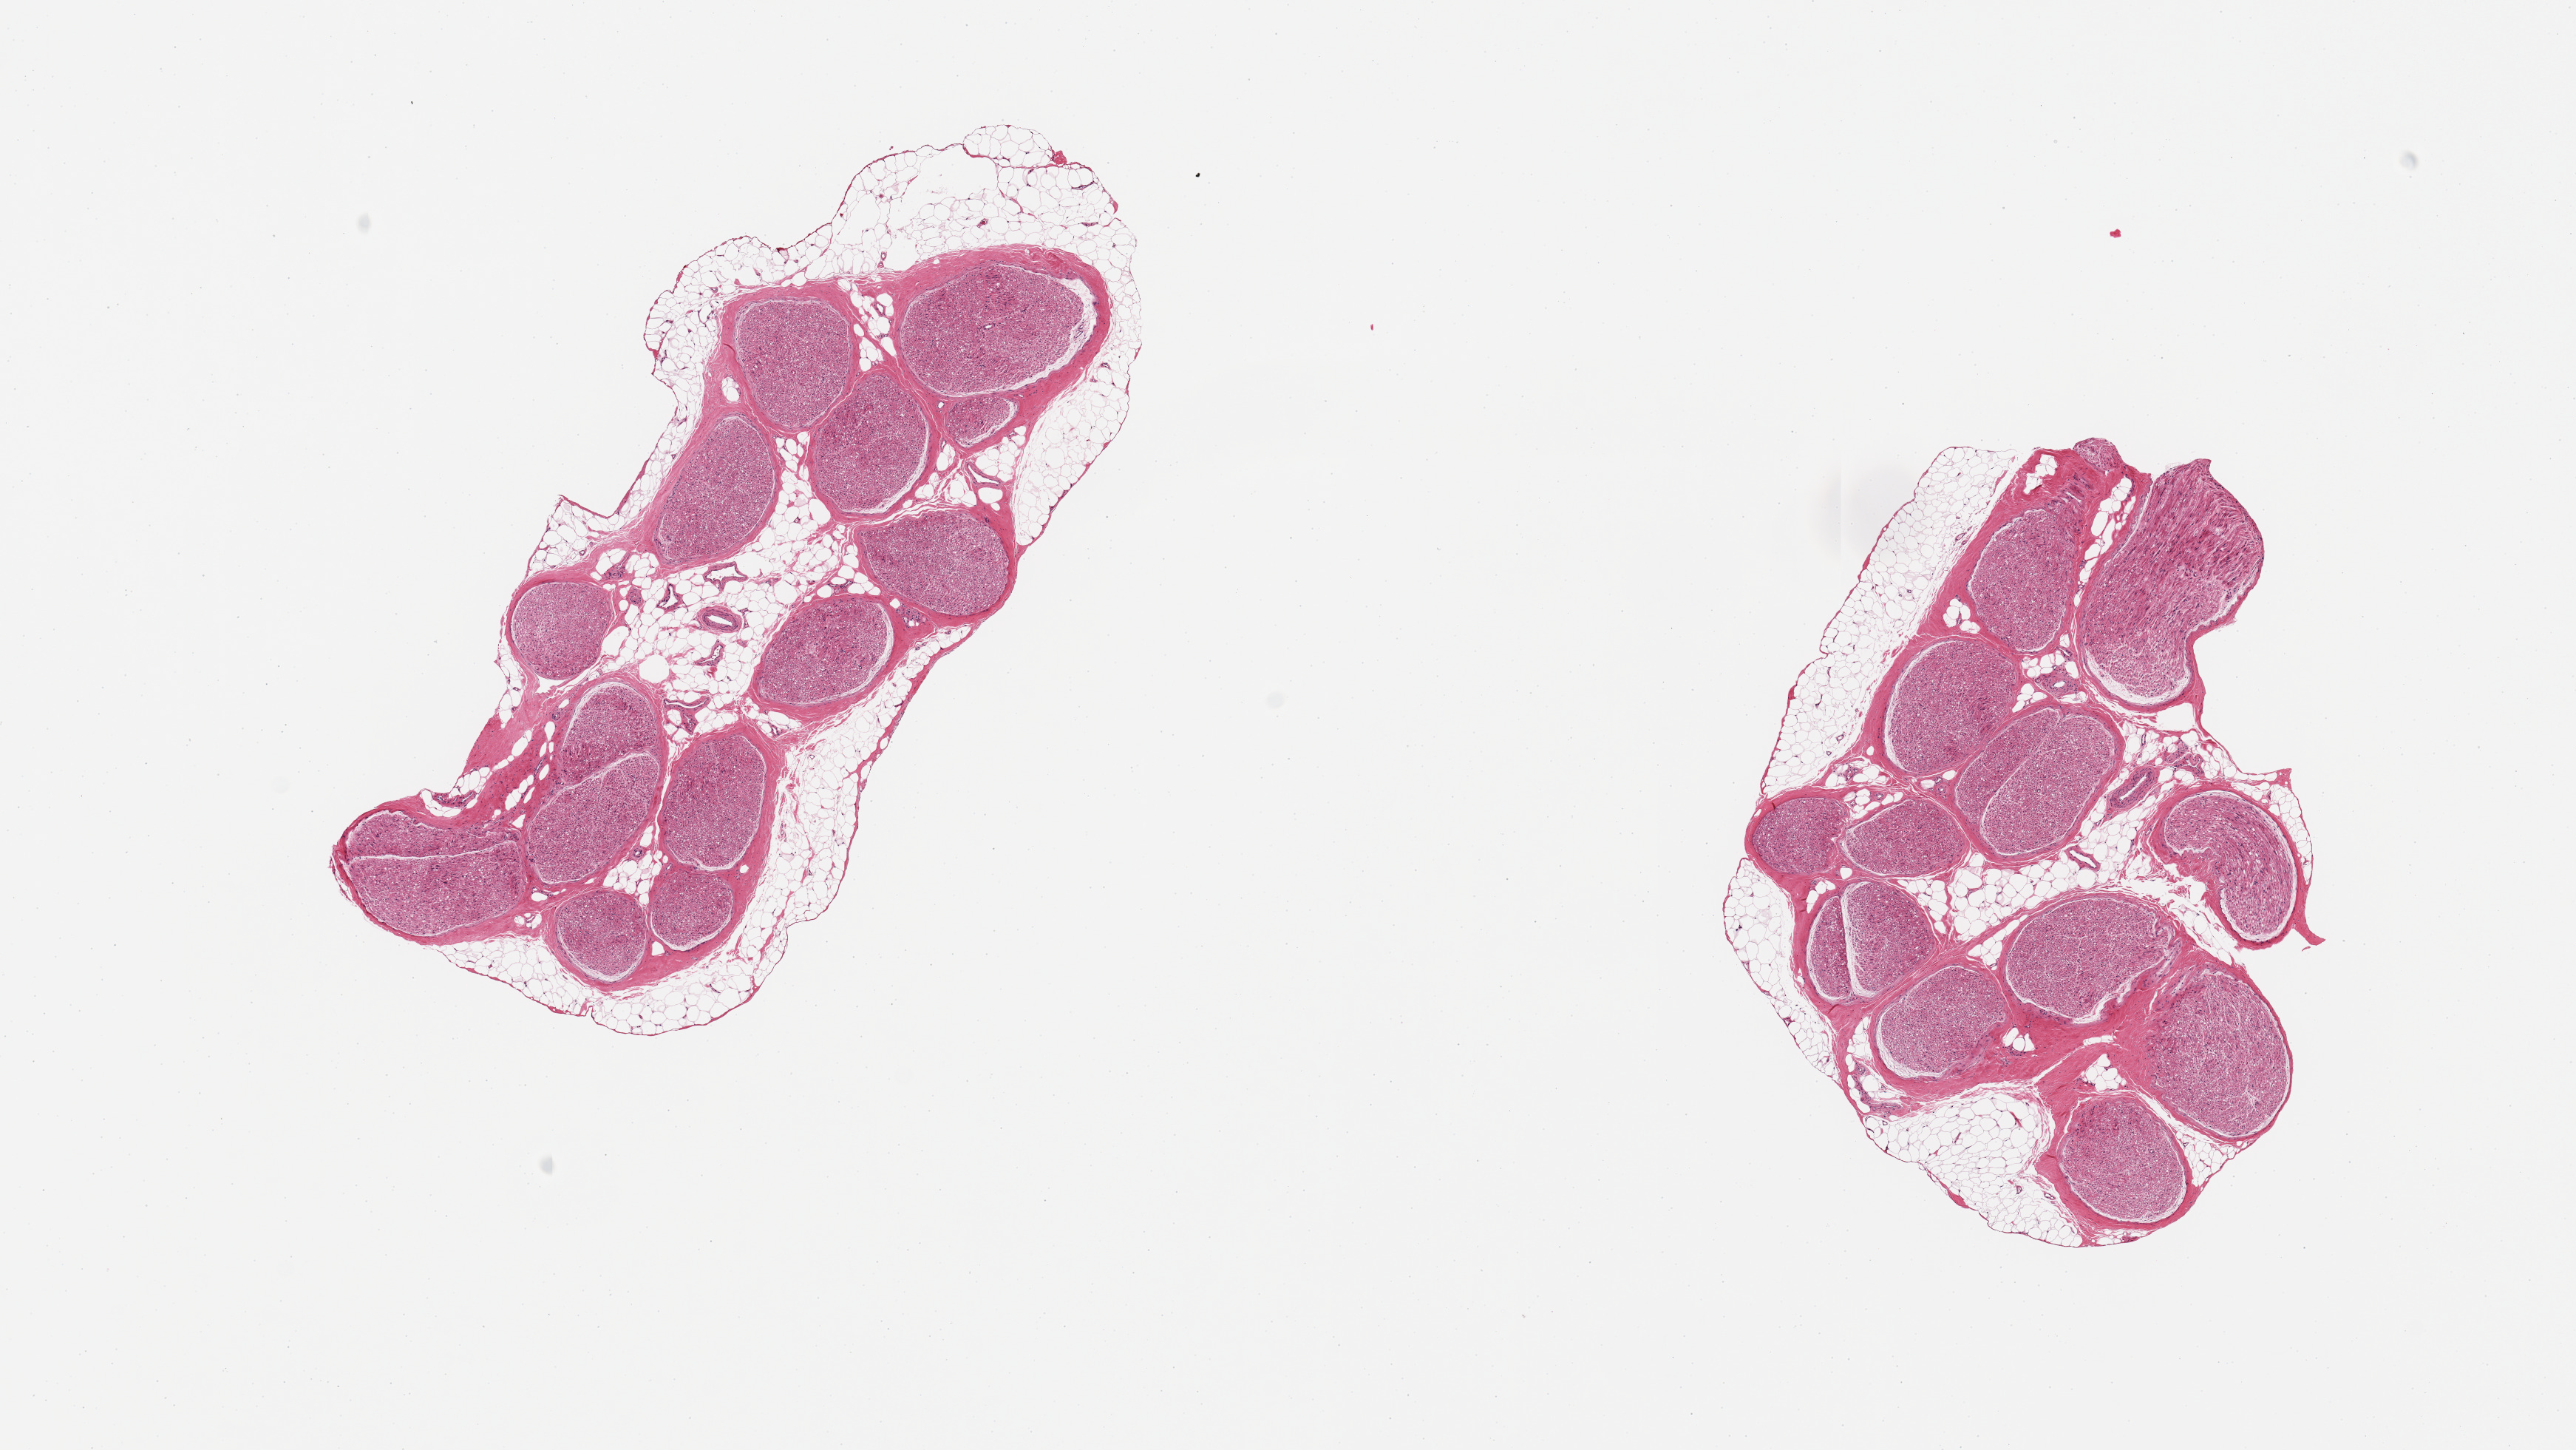
Digitized hematoxylin and eosin (H&E)-stained section — a low-resolution overview of the entire scanned area, about 13.8 x 7.8 mm (slide scanned at 20x); PAXgene-fixed paraffin-embedded (PFPE) section; sampled site (target tissue): tibial nerve; tissue donor sample. Donor sex: female.
Reviewer comment on this tissue sample: 2 pieces partial rims of fat, up to ~0.5mm.